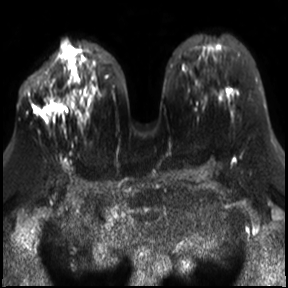
Breast MRI, one axial slice; position 16 of 30 along the scan axis; diffusion-weighted series; image 2 of 4 stored at this slice position (different b-values; order by instance number); 3 T; 4 mm slice thickness; 288 × 288 image matrix, field of view 340 × 340 mm. Female patient.
Annotated regions visible in this slice (manually delineated by an expert):
- tumour on diffusion-weighted imaging: bounding box [x1, y1, x2, y2] px = [41, 108, 51, 121]